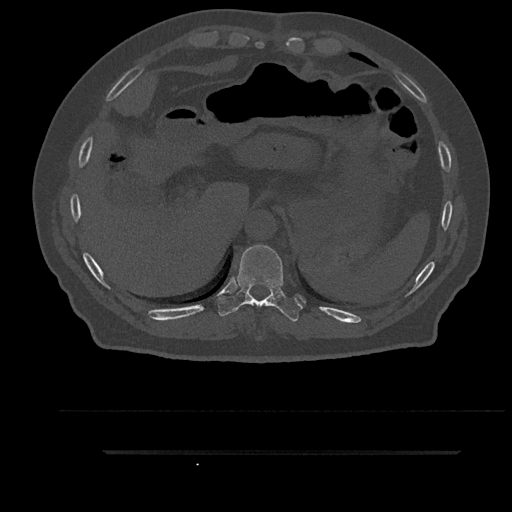
CT including the spine, one axial slice. Position 376 of 797 along the scan axis. Reconstruction kernel Br40s/3. Bone window (W 1800 / L 400 HU). 512 × 512 image matrix, field of view 432 × 432 mm. Male patient, age 63 years. From the clinical record (not read from this slice): primary cancer: renal; vertebrae with lytic lesions (as recorded): T8.
Structures marked on this image (semi-automatically segmented with operator editing):
- T10 vertebra: bounding box <218,245,303,322> (left, top, right, bottom; pixels)